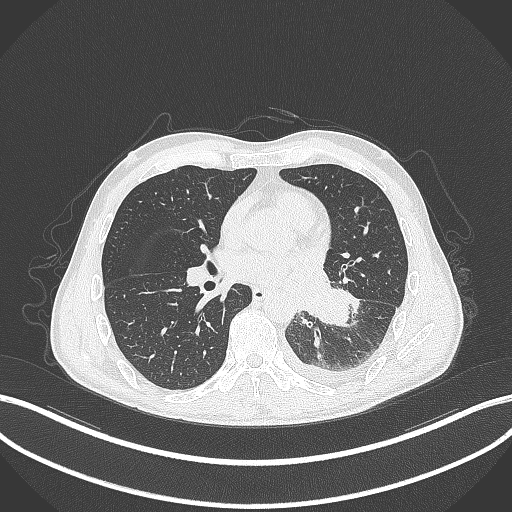
Chest CT, one axial slice. Position 149 of 295 along the scan axis. Lung window (W 1500 / L -600 HU). 1 mm slice thickness. 512 × 512 image matrix. Patient: male, 47 years. From the clinical record (not read from this slice): clinical TNM (as recorded): T3 N1 M1c; histopathological grade: G3.
Structures marked on this image (rectangle marked by the reading radiologist):
- lung tumour (recorded histology: small cell carcinoma): bounding box (x1, y1, x2, y2) in pixels: (305, 288, 350, 329)